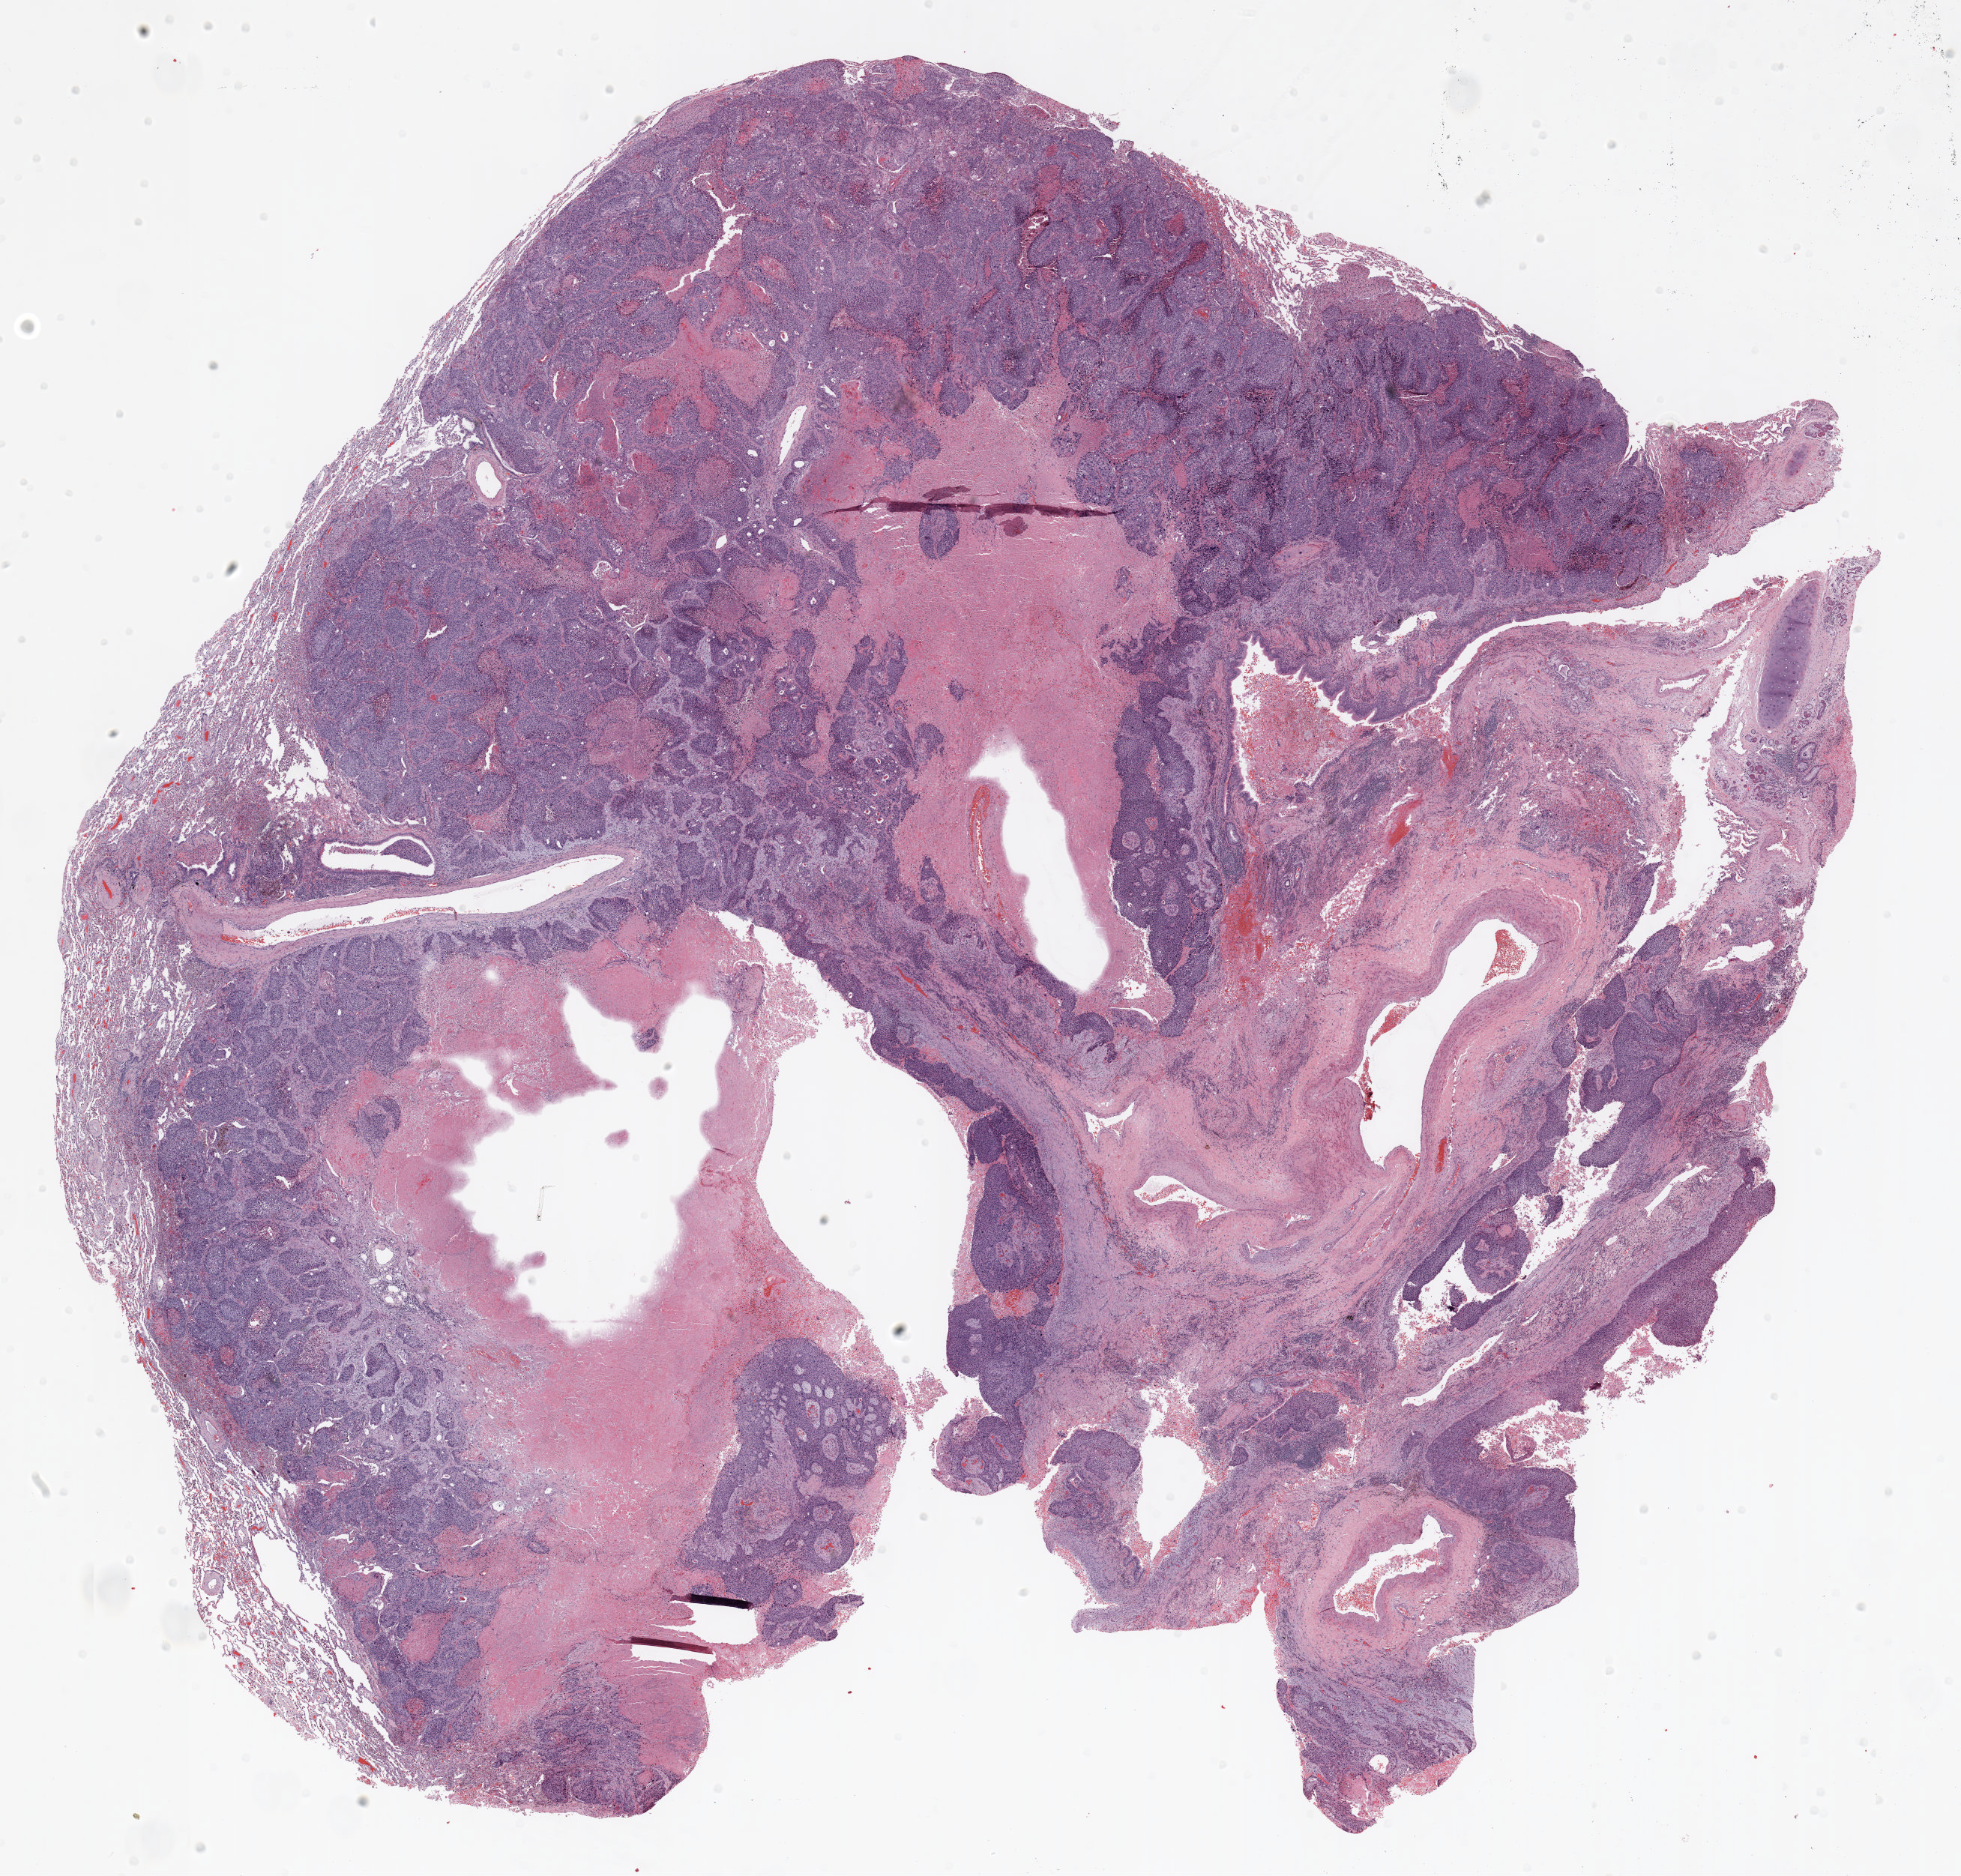
H&E whole-slide image, shown as a low-resolution overview of the whole scanned area (about 21.0 x 20.1 mm, from a 20x scan). Formalin-fixed paraffin-embedded (FFPE) section. Lung. Male patient, aged 60 at enrolment. Current smoker at enrolment.
Participant's lung-cancer diagnosis: Squamous cell carcinoma, NOS.